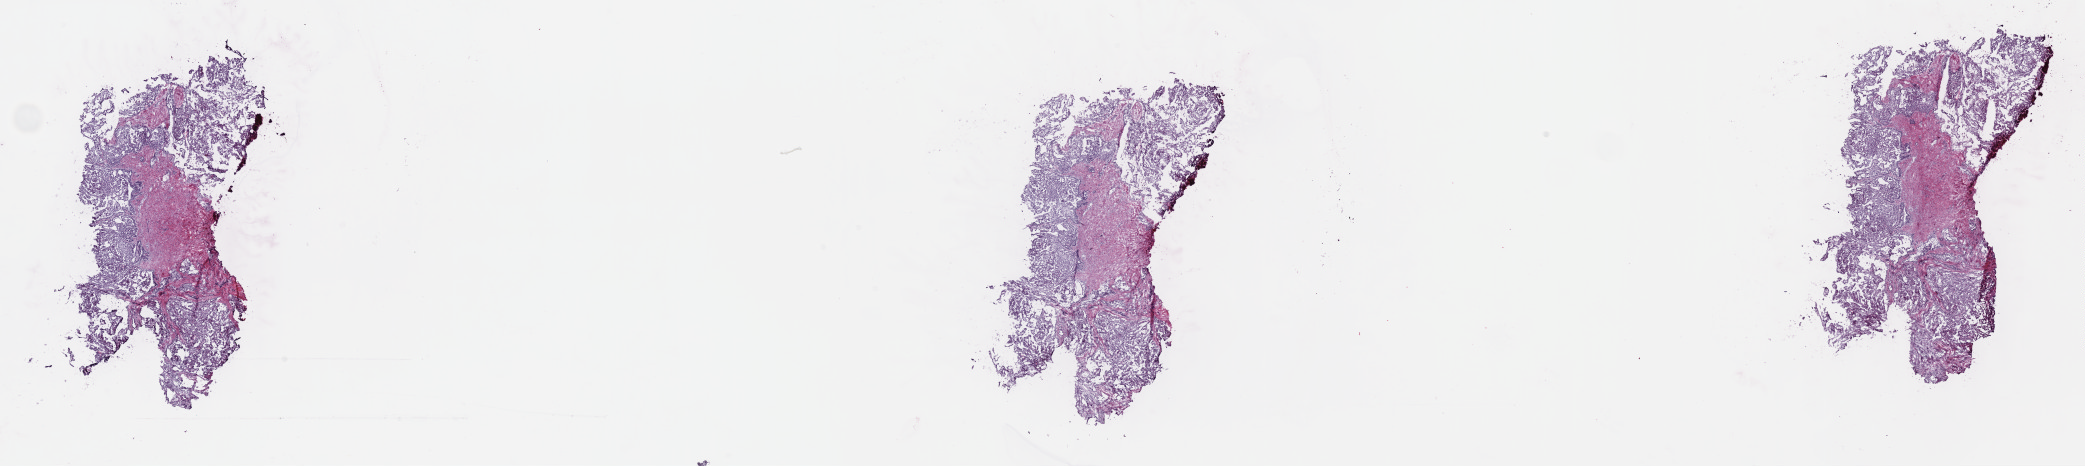
Digitized H&E-stained tissue section (whole slide) — a low-resolution overview of the entire scanned area, about 33.7 x 7.5 mm, frozen section, kidney, primary tumour sample. Female, age 68 years at initial diagnosis. Composition of this section per pathologist review: tumour cells 70%, tumour nuclei 70%, normal cells 0%, stromal cells 30%, necrosis 0%. Inflammatory infiltration, as recorded: lymphocyte infiltration 2%, monocyte infiltration 3%, neutrophil infiltration 1%.
Histologic diagnosis: Papillary adenocarcinoma, NOS. Laterality: left. TNM: T1a N0 MX. AJCC pathologic stage: I (7th edition).